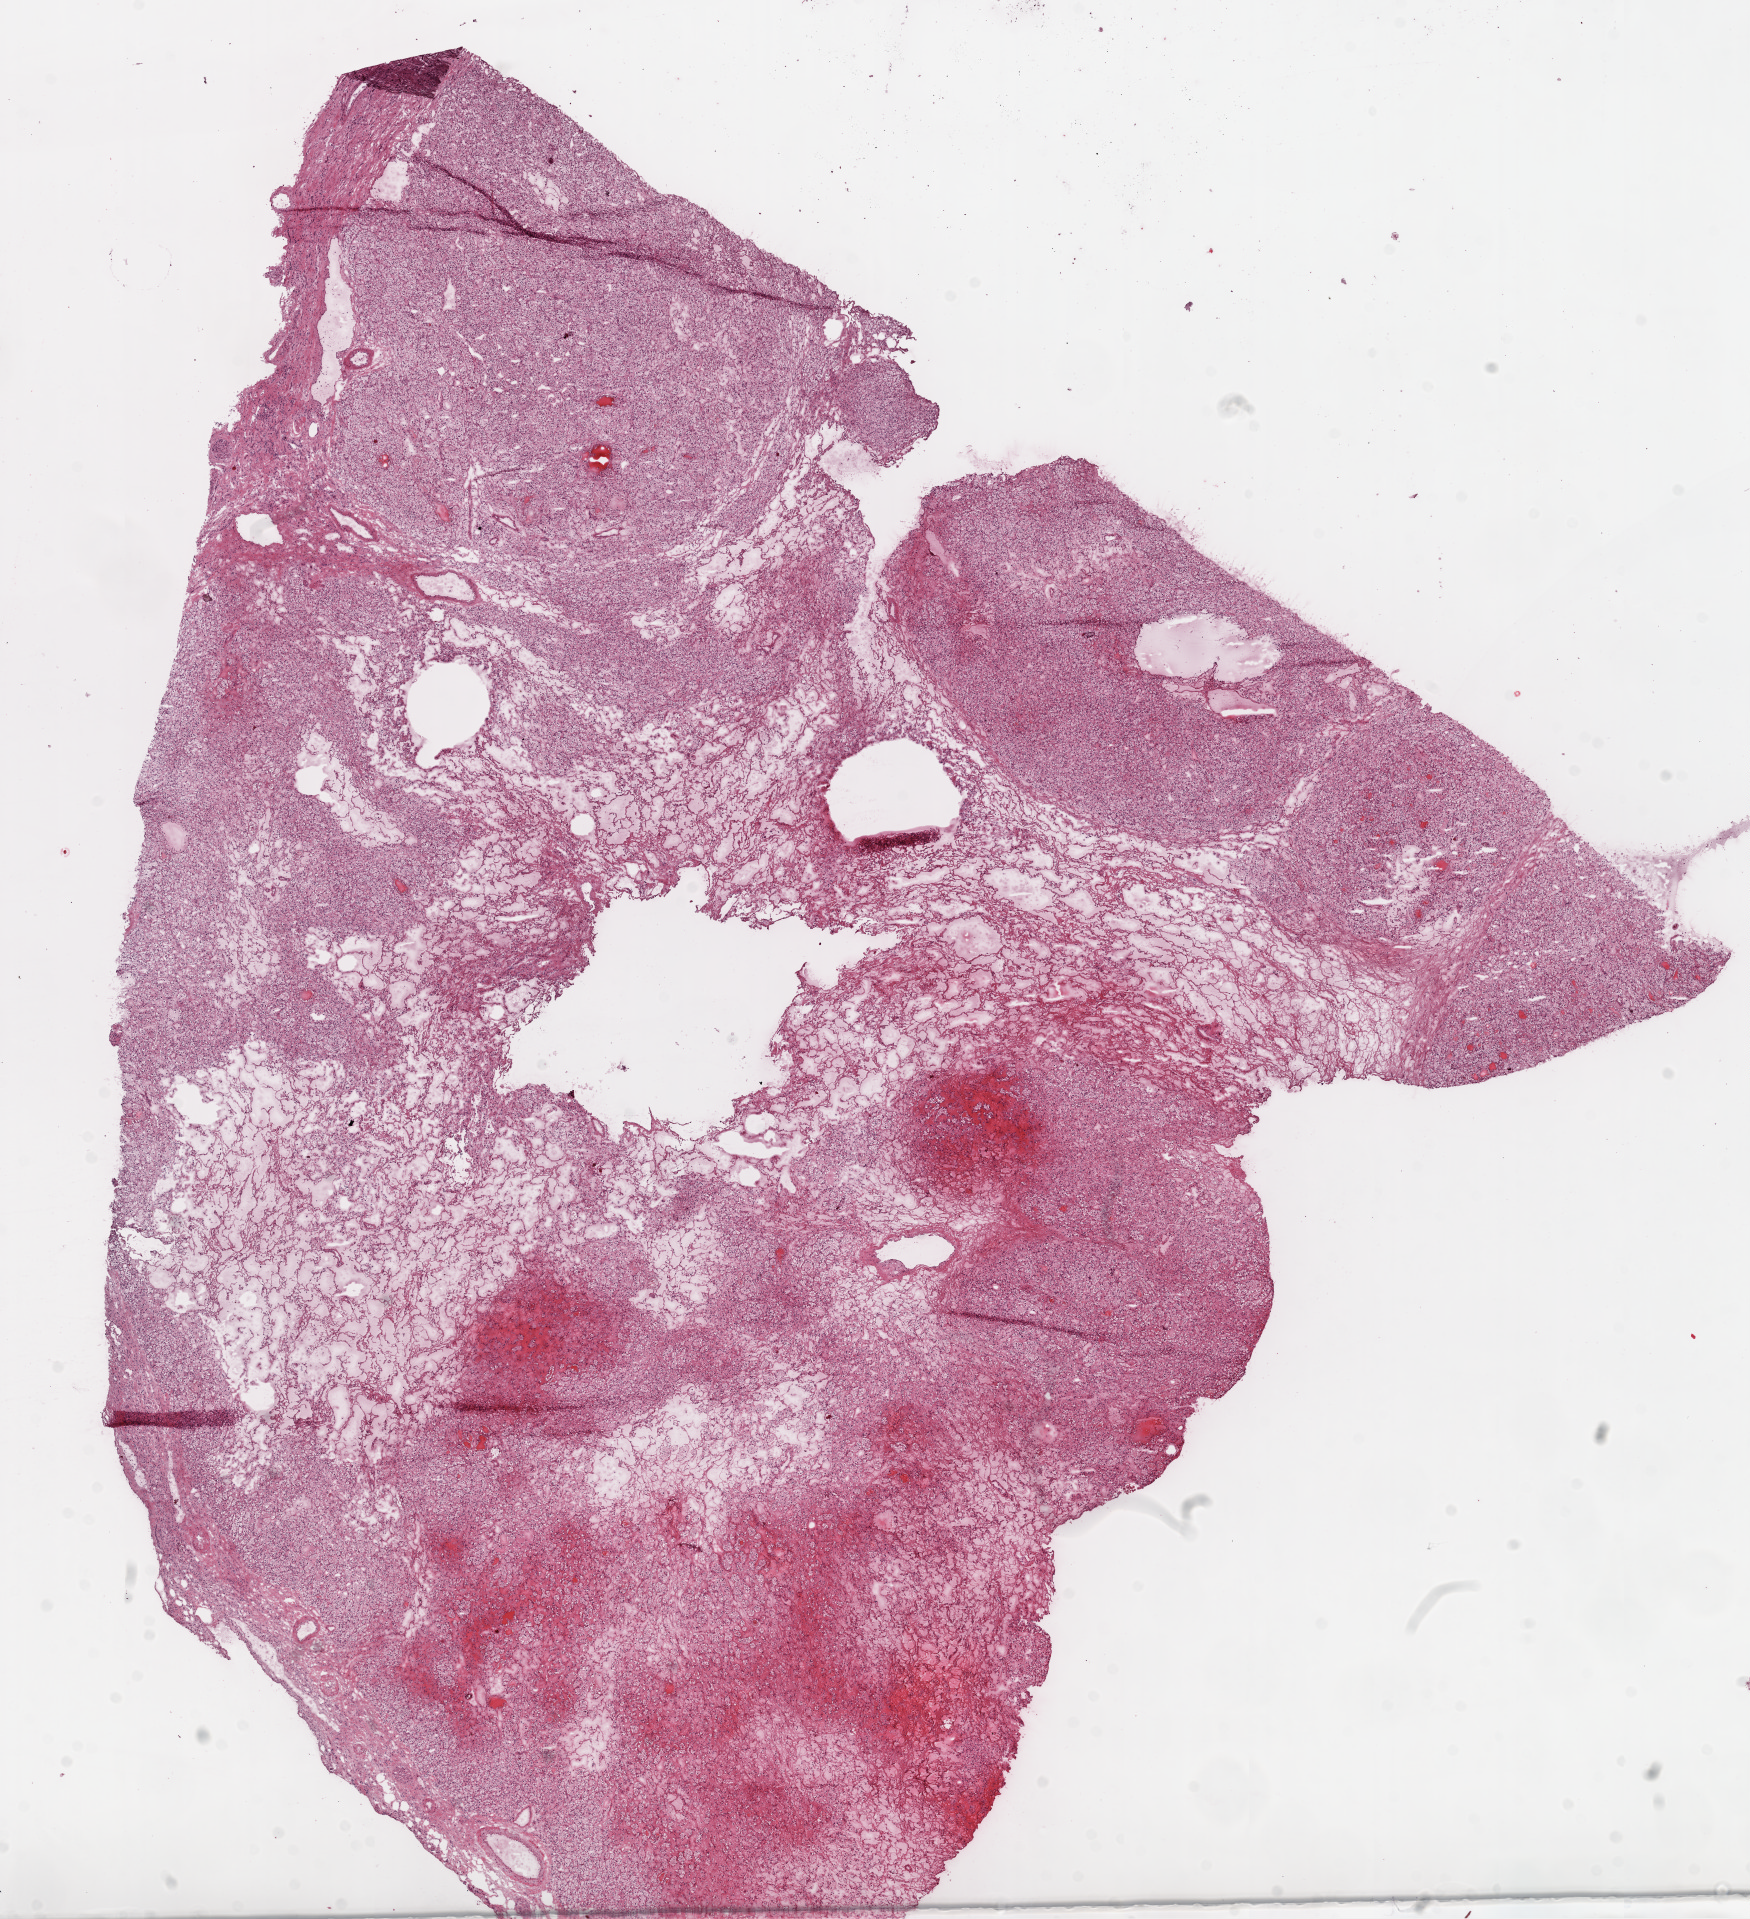
Digitized H&E tissue section (whole slide), low-resolution overview of the scanned area, about 14.0 x 15.4 mm (from a 20x scan); frozen section from the top of the tissue portion; sample: primary tumour, kidney. Patient: male, age at initial diagnosis 43 years. Histologic grade: G2 (moderately differentiated). Pathologist review of this section (percent, as recorded): tumour cells 95%, tumour nuclei 90%, stromal cells 5%, necrosis 0%. Inflammatory infiltration, as recorded: lymphocyte infiltration 1%.
Laterality: right. Diagnosis: Clear cell adenocarcinoma, NOS. AJCC pathologic stage: I.